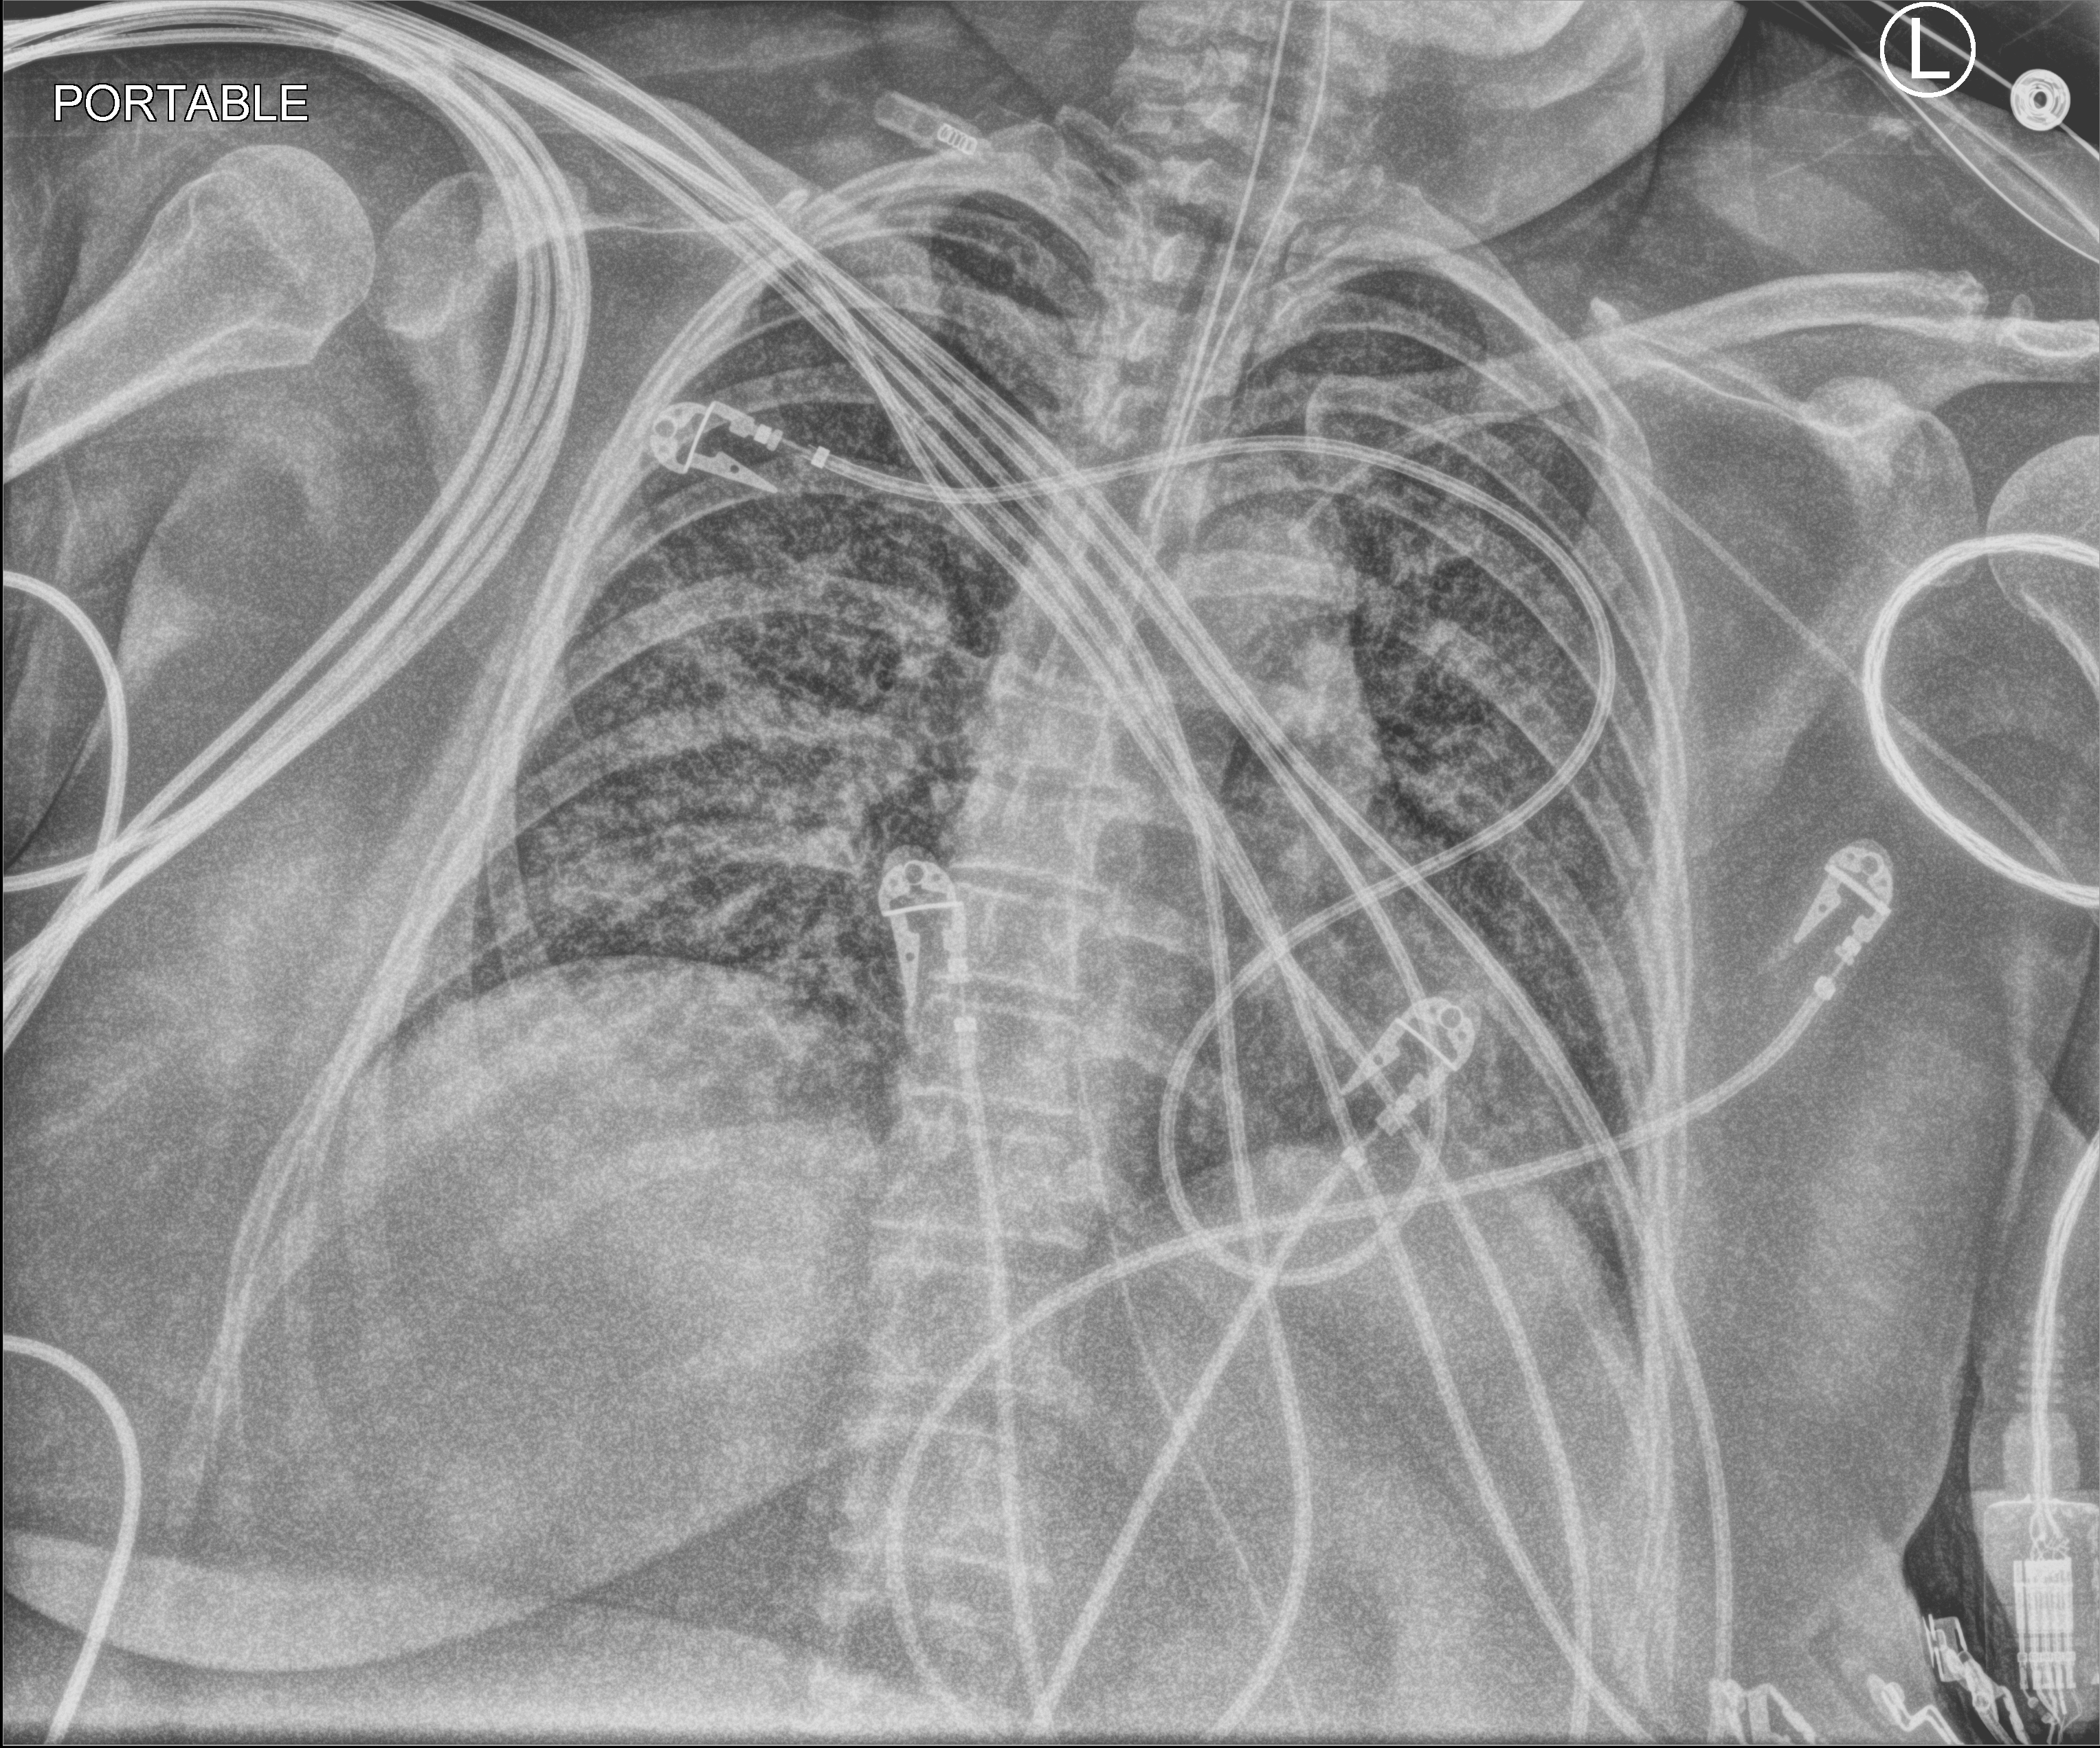
Portable chest radiograph, anteroposterior (AP) projection. Patient hospitalised with COVID-19; female, aged 18–59 years.
From the hospital-stay record, not from the radiograph (when in the stay this image was taken is not recorded): hypertension (admission record): yes.